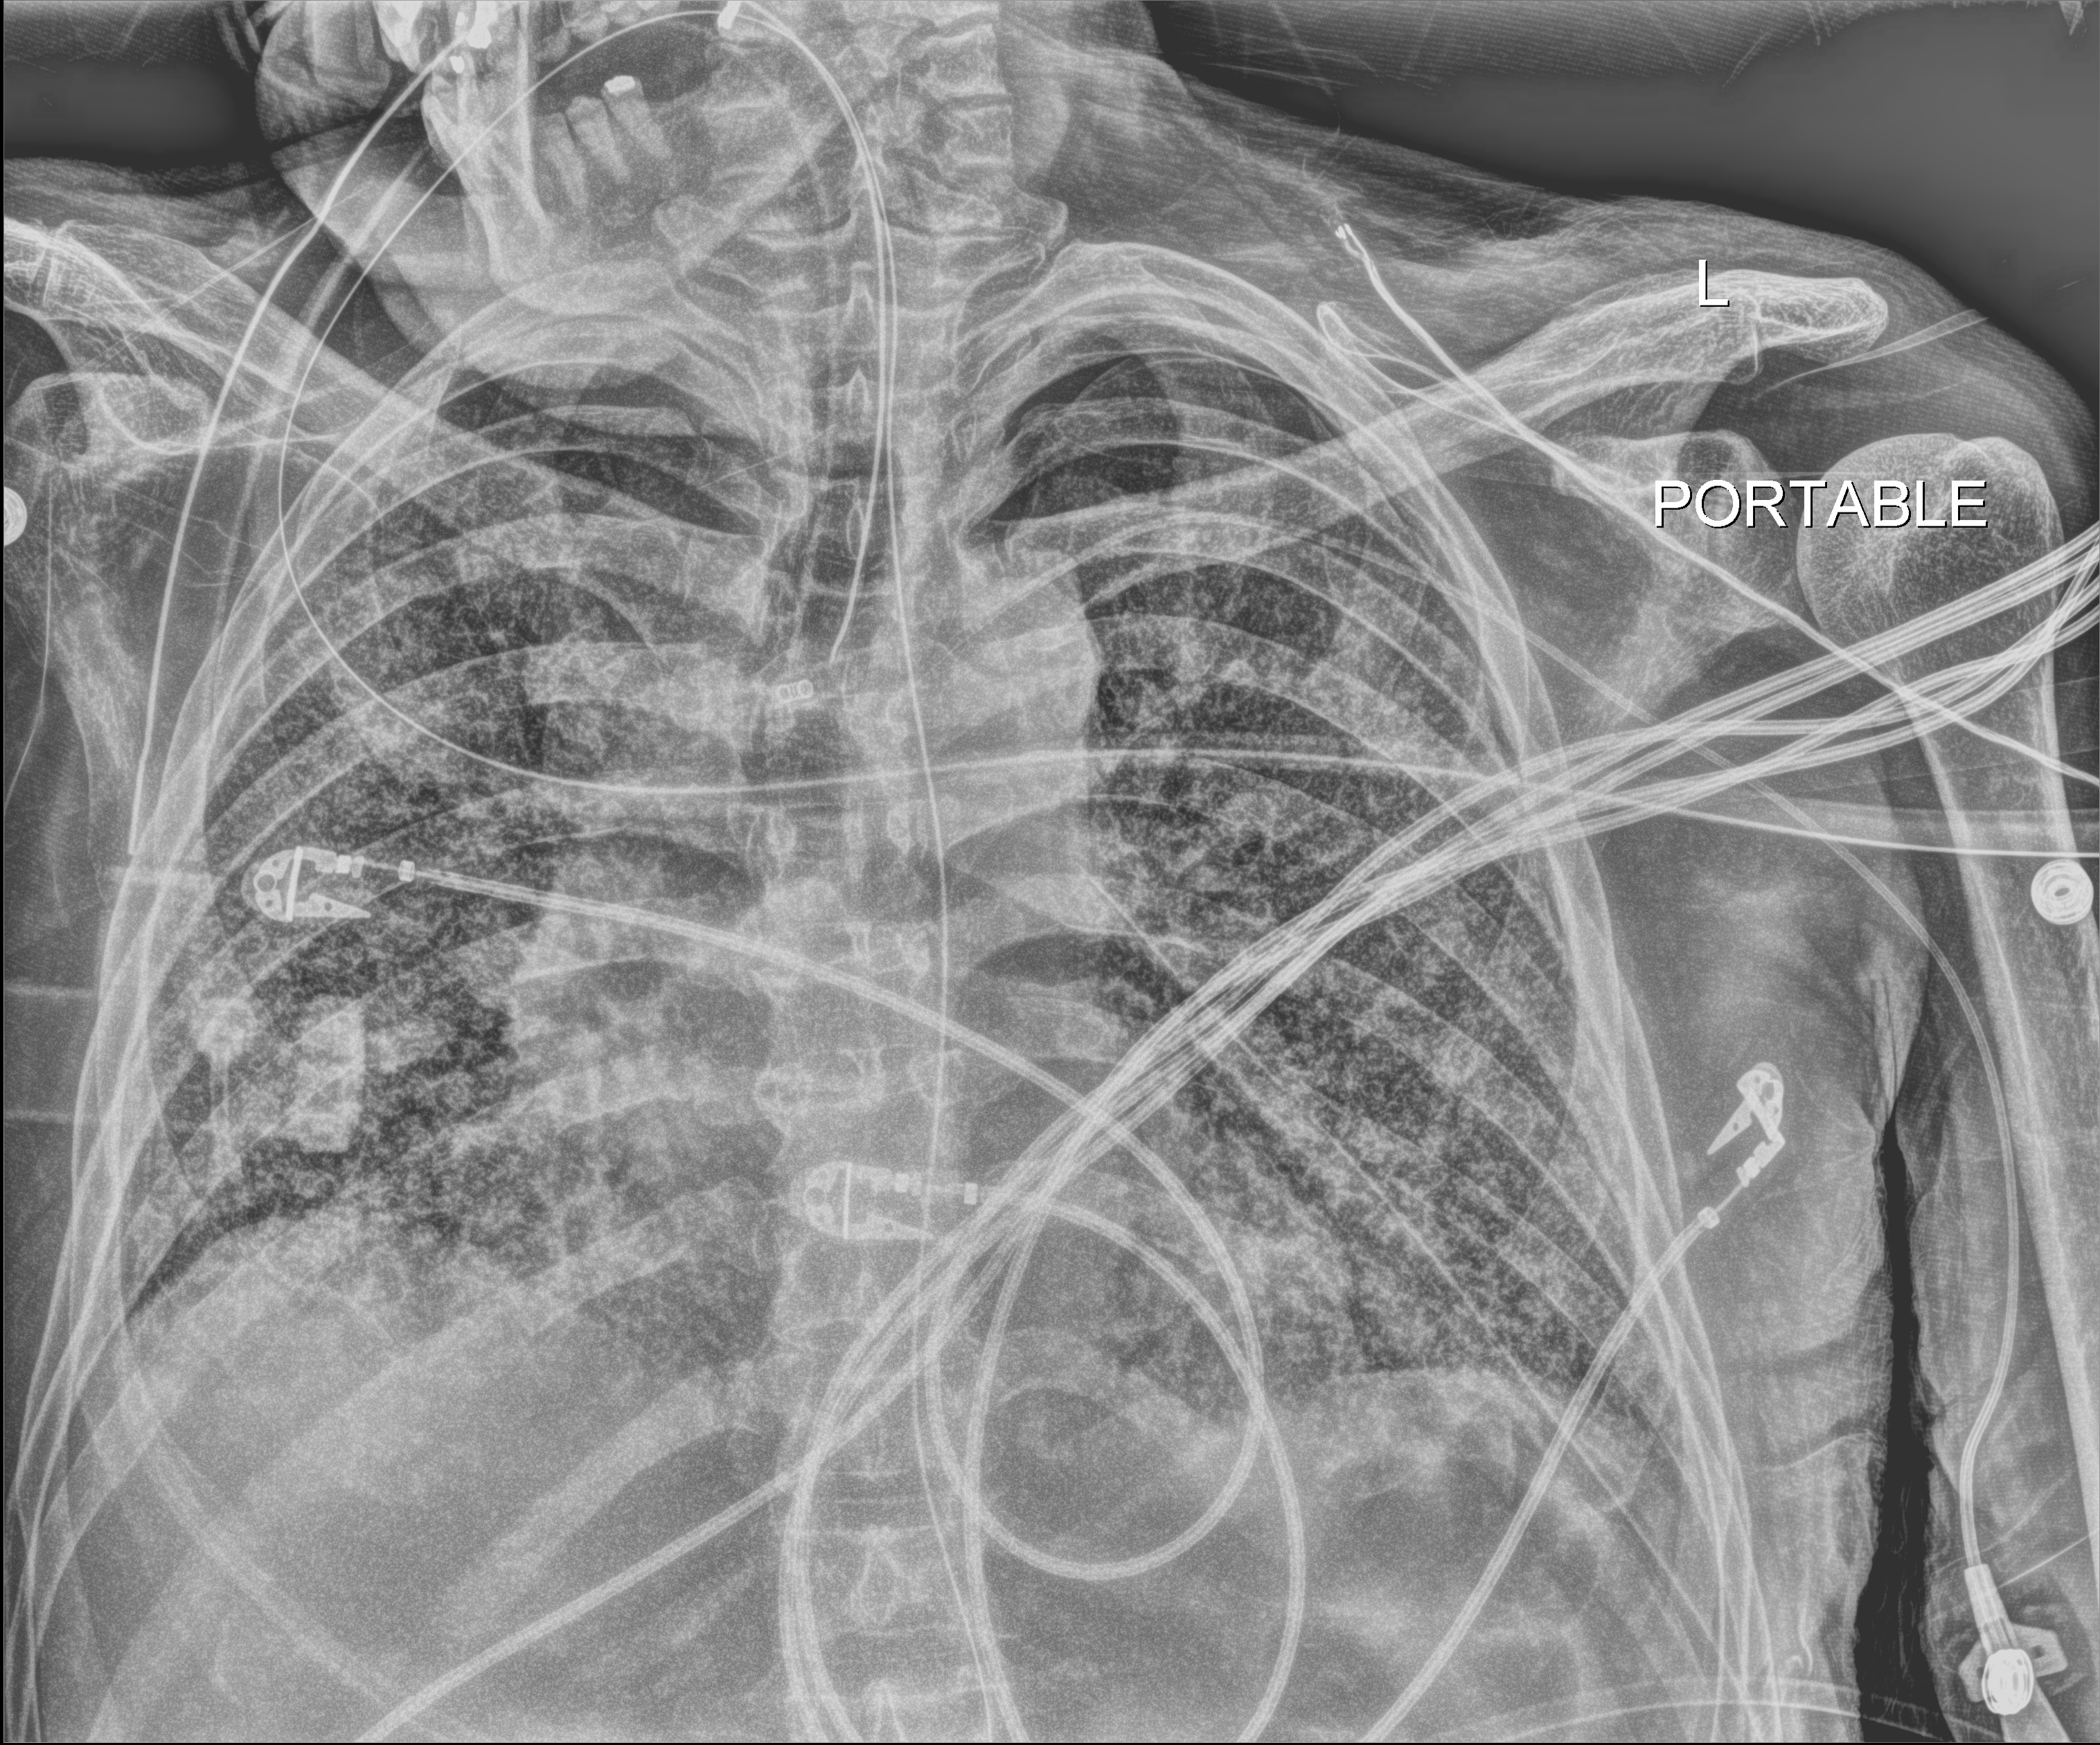
Bedside chest radiograph (digital radiography); anteroposterior (AP) projection. Male patient hospitalised with COVID-19, age 60–74 years.
Hospital-stay facts (about this admission, not read from this image; timing relative to this image not recorded):
- mechanically ventilated during this hospital stay: yes
- length of hospital stay: 54 days